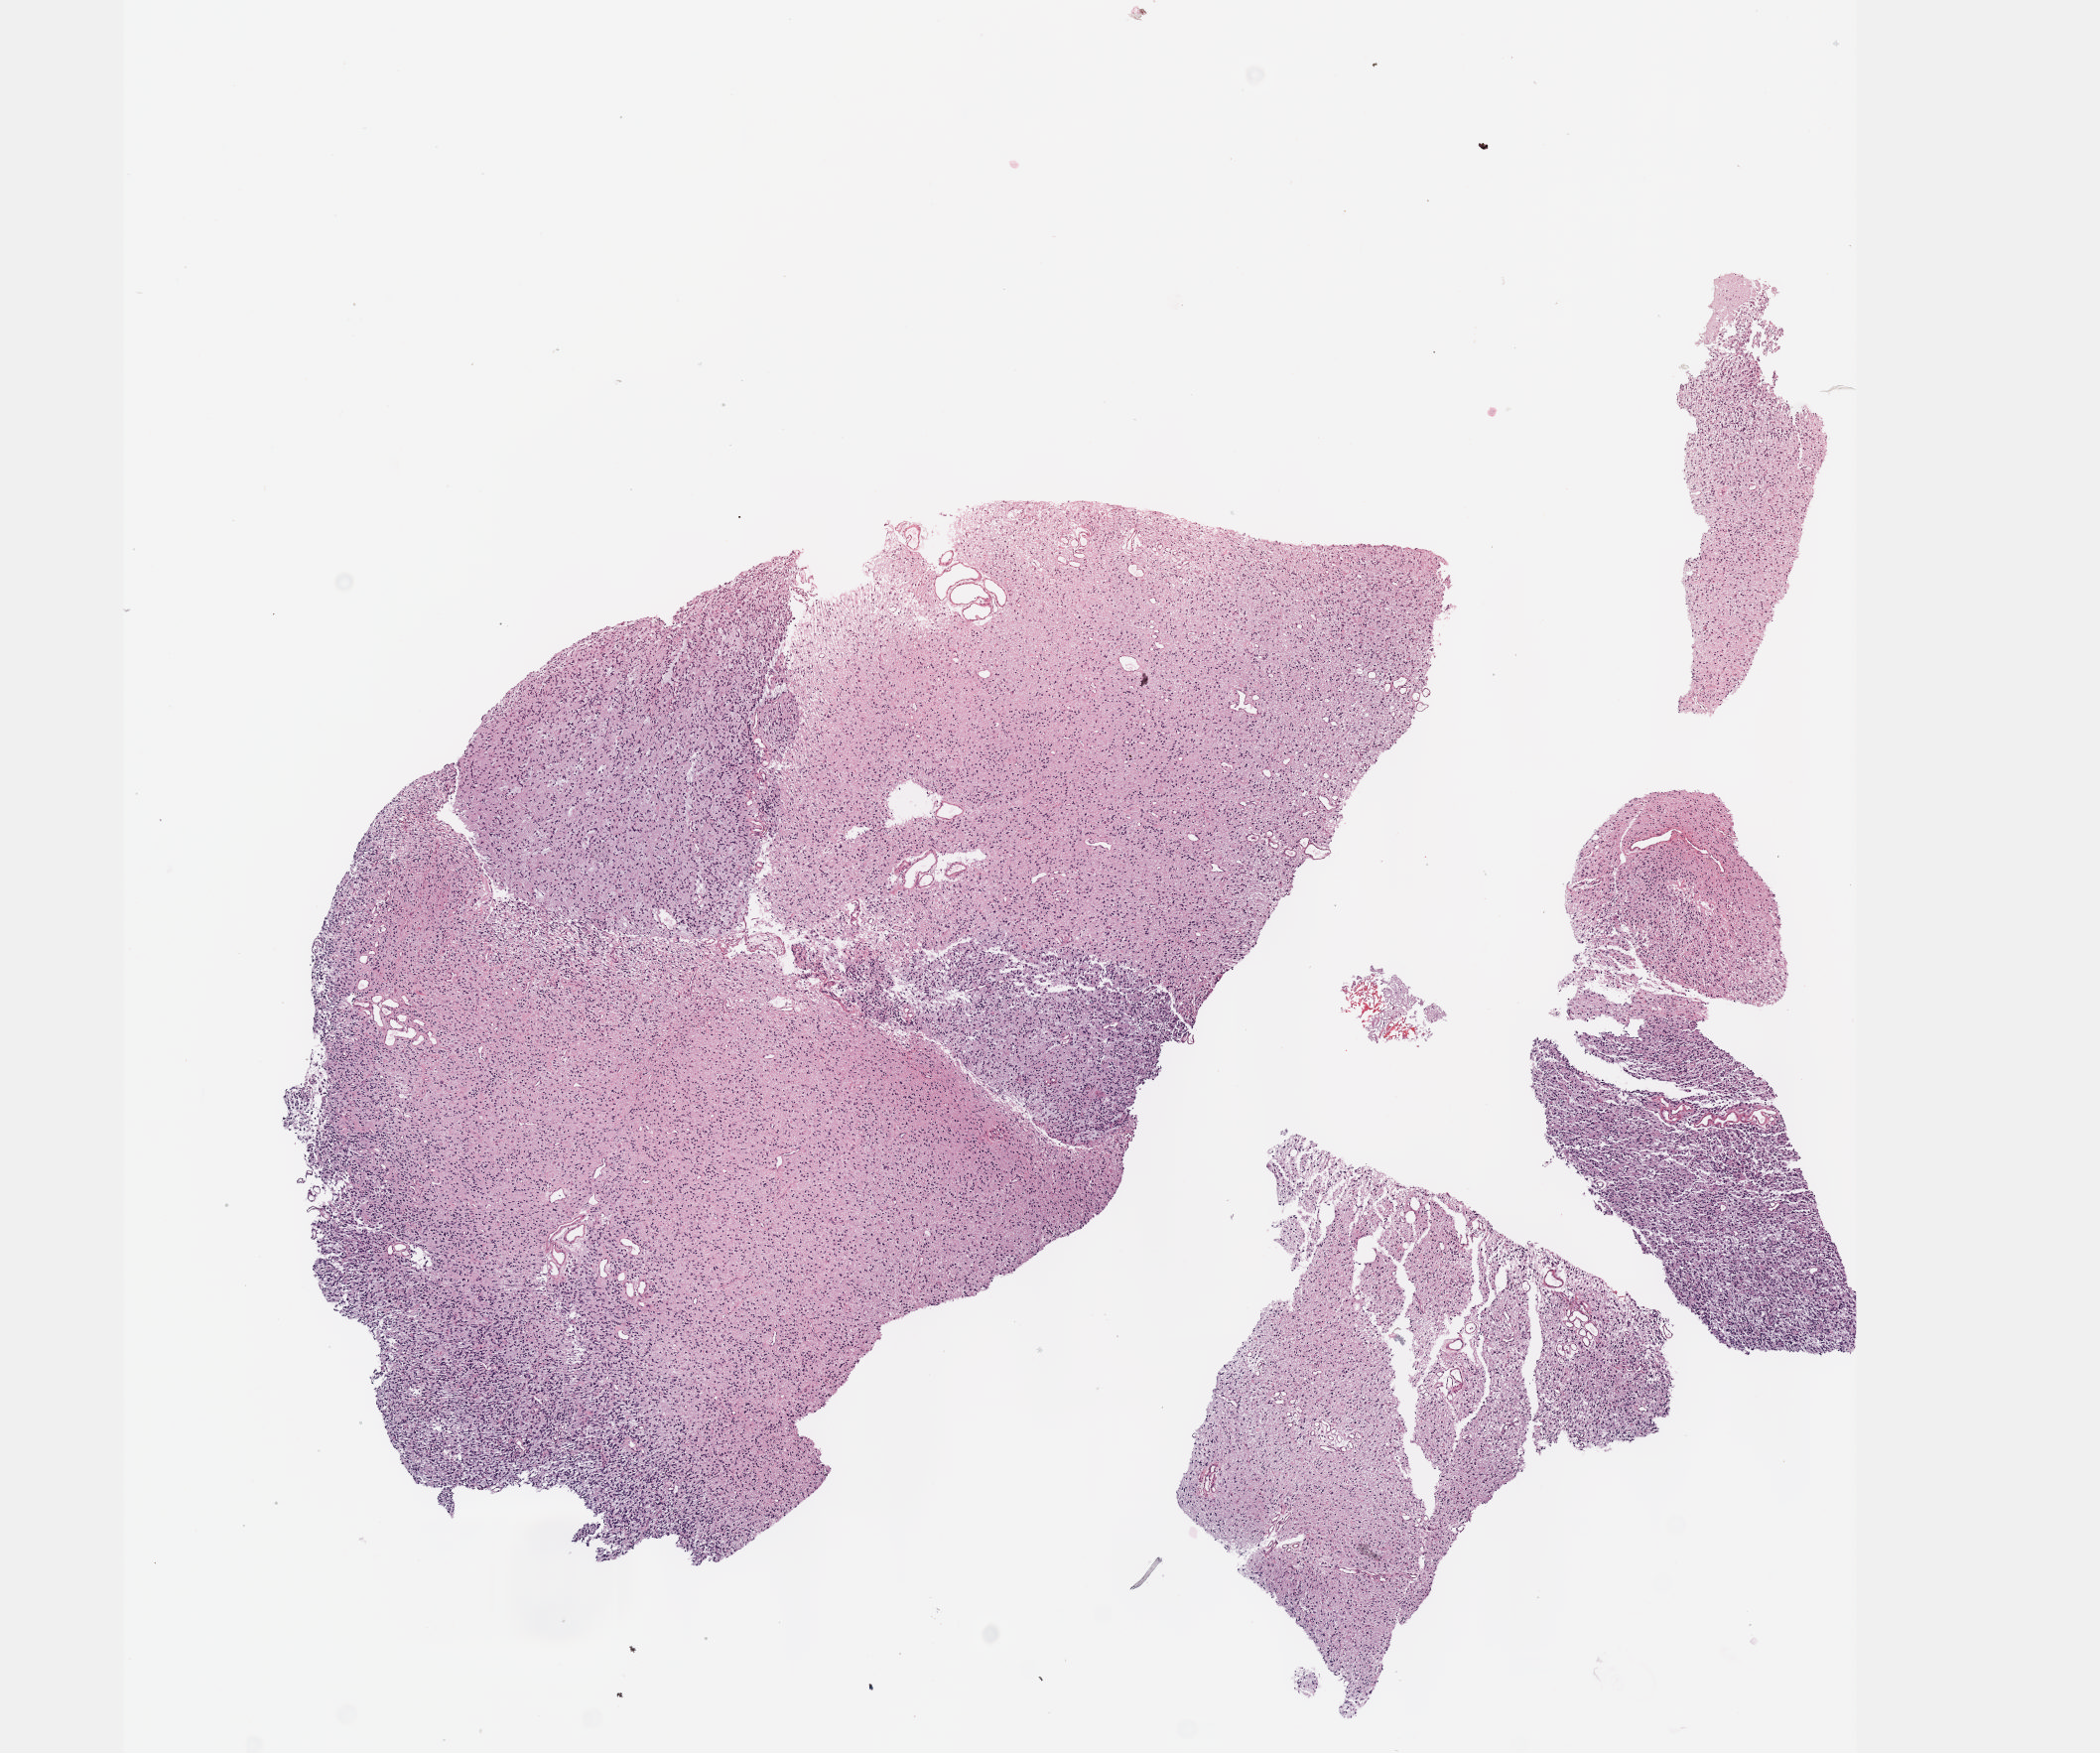
H&E whole-slide image, low-resolution overview of the scanned area, about 8.6 x 7.1 mm (acquisition: 40x scan). FFPE section. Sample: primary tumour, brain. Male patient; age at initial diagnosis 59 years.
Pathologic diagnosis: Oligodendroglioma, NOS.